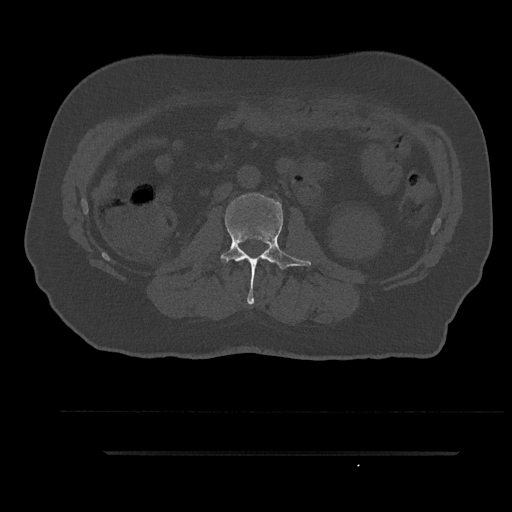
CT including the spine, one axial slice; slice 107 of 797 in the series (ordered by position); reconstruction kernel Br40s/3; bone window (W 1800 / L 400 HU); 0.5 mm slice thickness; 512 × 512 image matrix. Patient: male, 63 years. Case-level facts recorded for this patient, not image findings: primary cancer: renal.
Structures marked on this image (semi-automatically segmented with operator editing):
- L2 vertebra: bounding box <220,194,311,305> (left, top, right, bottom; pixels)